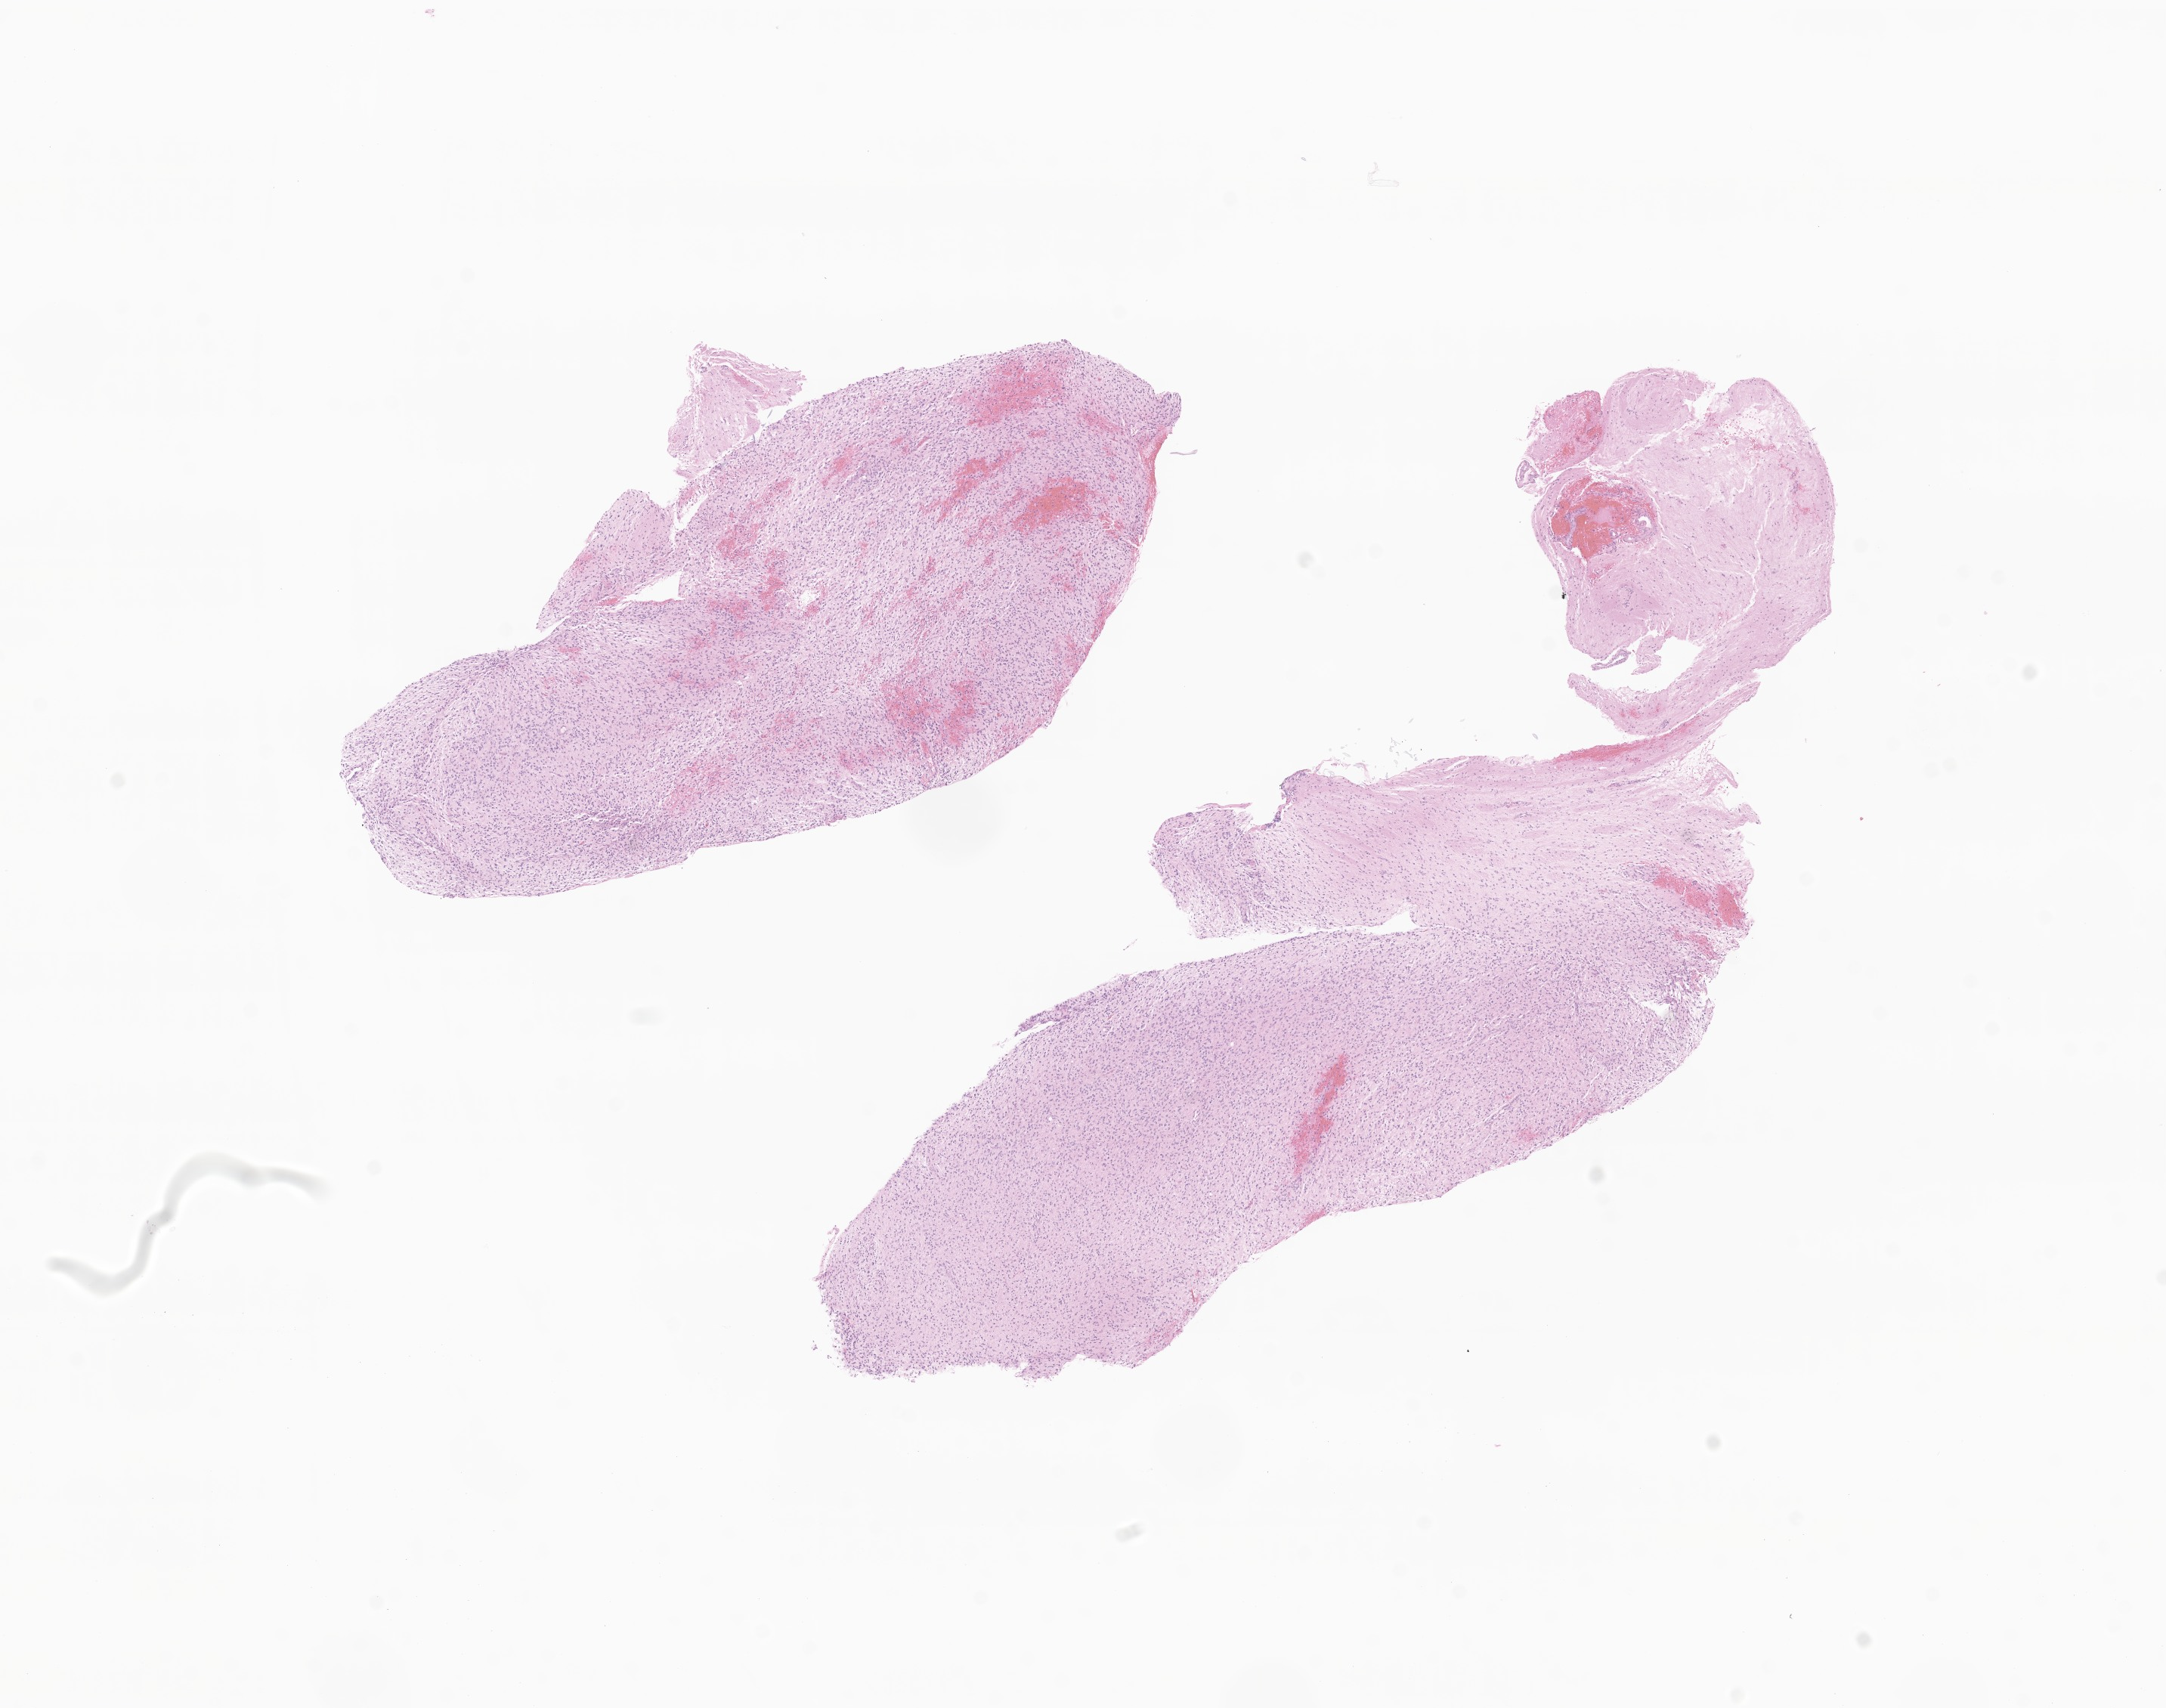
Whole-slide image, hematoxylin and eosin (H&E) stain of tumor tissue from the brain — a low-resolution overview of the entire scanned area, about 12.1 x 9.5 mm; FFPE section. Patient: female, age 124 months (10 years 4 months).
* recorded diagnosis: Glioma, malignant